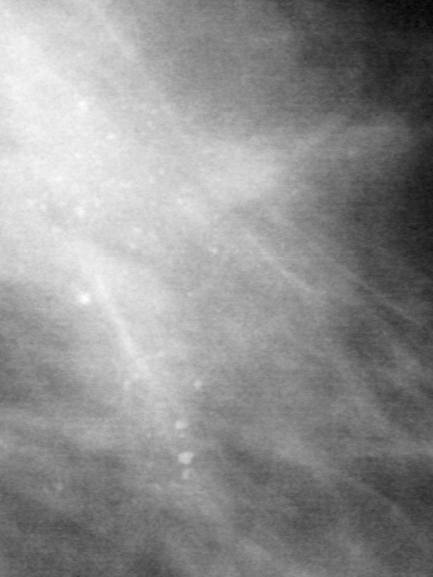
Region of interest cut from a scanned film mammogram (one marked finding), right breast, MLO view.
Calcifications, morphology pleomorphic, distribution clustered; BI-RADS assessment category 4; subtlety rating 4 on a 1 (subtle) to 5 (obvious) scale; pathology (as recorded): malignant.